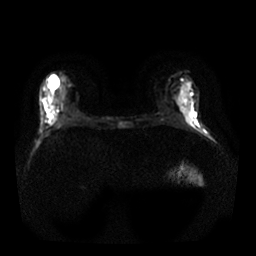
Breast MRI, one axial slice; slice 10 of 25 in the series (ordered by position); diffusion-weighted series; image 2 of 4 stored at this slice position (different b-values; order by instance number); 1.5 T; 256 × 256 image matrix, field of view 340 × 340 mm. Female patient.
Annotated regions visible in this slice (outlined manually by an expert reader):
- tumour on diffusion-weighted imaging: bounding box <62,104,72,114> (left, top, right, bottom; pixels)